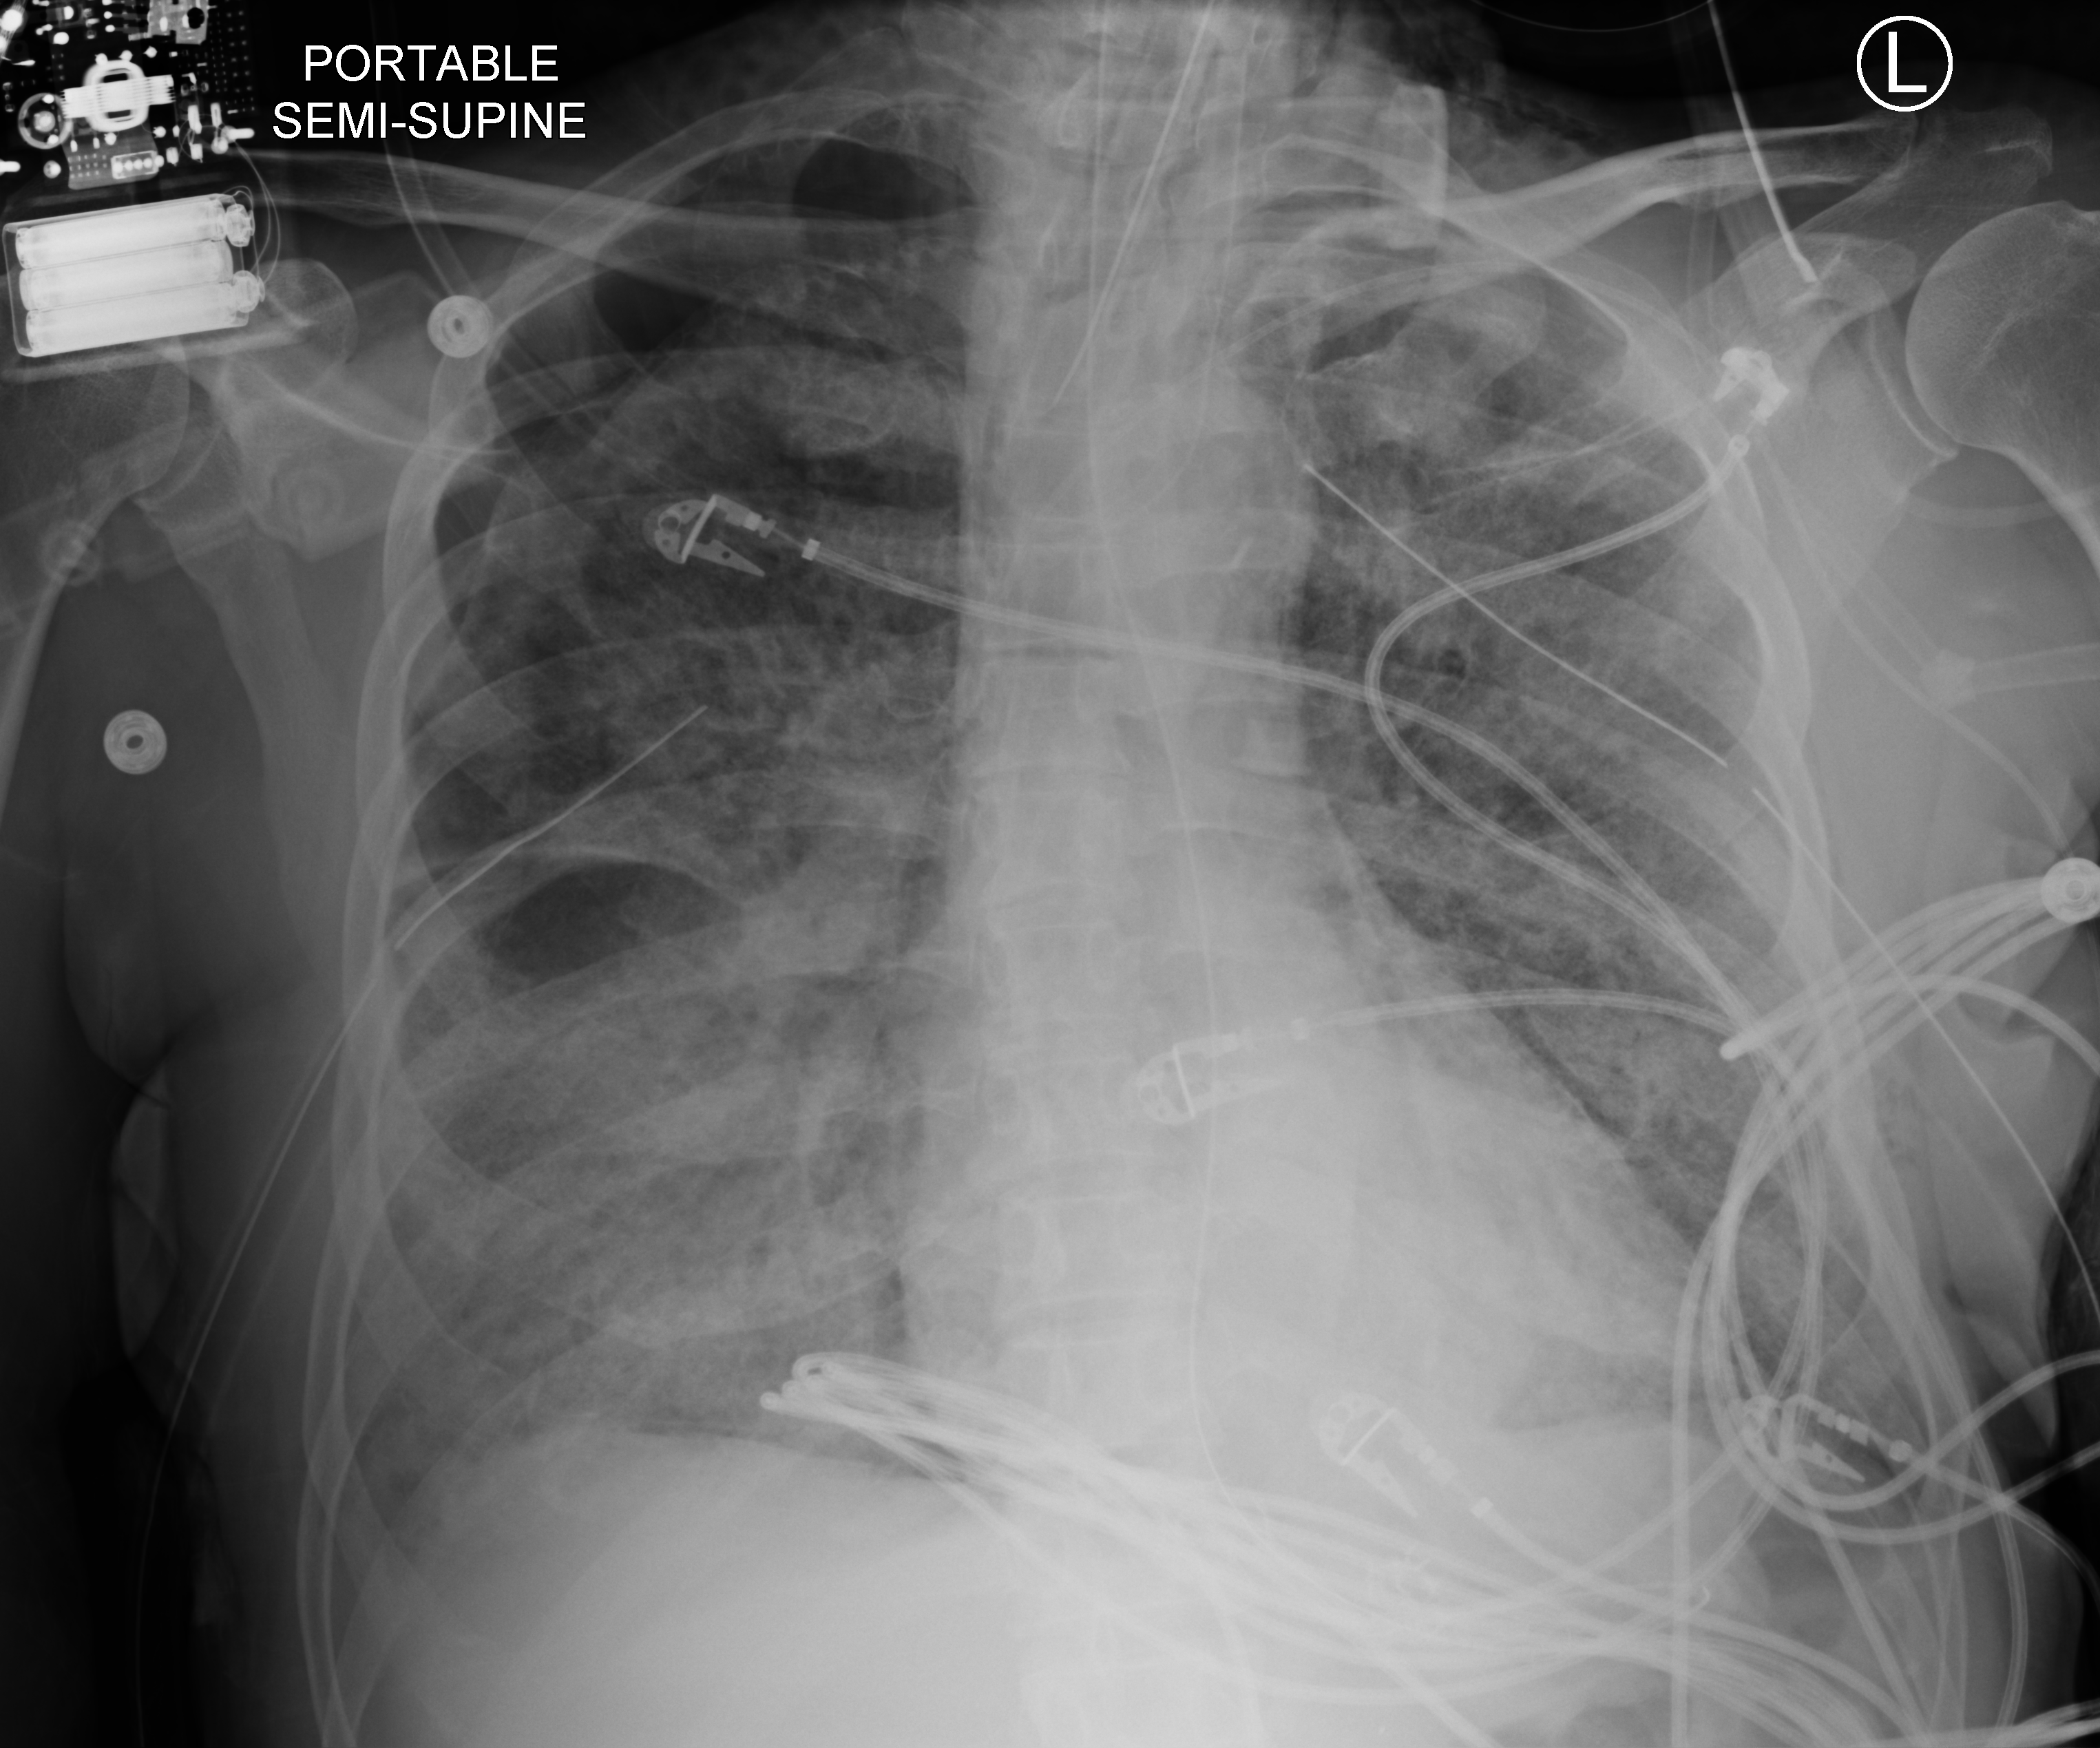
Portable chest radiograph. Patient hospitalised with COVID-19; male, aged 60–74 years.
Admission-level facts for this patient (not findings on this image; timing relative to this image not recorded): mechanically ventilated during this hospital stay: yes; smoking status (admission record): former; length of hospital stay: 31 days.